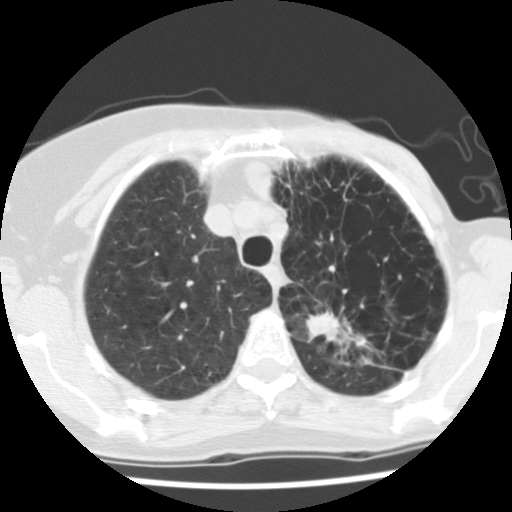
Axial slice from a low-dose chest CT screening exam; baseline annual screen; lung window (W 1500 / L -600 HU); 2.5 mm slice thickness; standard (soft-tissue) reconstruction kernel (STANDARD); 140 kVp. Female, age 67 years at enrolment. Current smoker at enrolment.
Lesion marked by an expert reader, bounding box <294,293,386,373> (left, top, right, bottom; pixels). The screening reader recorded 2 non-calcified nodules or masses ≥4 mm on this exam (left upper lobe, left lower lobe); which of them this box marks is not recorded. Official screen result: positive, change unspecified: nodule(s) >= 4 mm or enlarging nodule(s), mass(es), or other non-specific abnormalities suspicious for lung cancer.